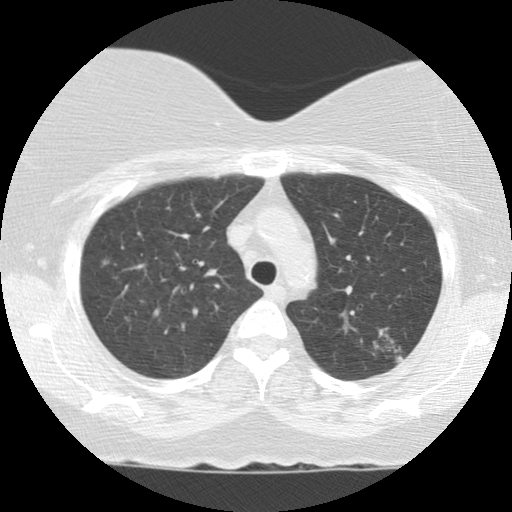
Chest CT (low-dose screening protocol), one axial image. Baseline annual screen. Lung window (W 1500 / L -600 HU). 2.5 mm slice thickness. Standard (soft-tissue) reconstruction kernel (STANDARD). Slice 27 of 123 in the series. Female participant, aged 56 years at enrolment. Current smoker at enrolment.
Expert-annotated lung lesion, box from (x=357, y=317) to (x=419, y=383) px. The screening reader recorded 4 non-calcified nodules or masses ≥4 mm on this exam (left upper lobe, left upper lobe, right upper lobe, left upper lobe); which of them this box marks is not recorded. Participant outcome: lung cancer diagnosed 798 days after this screen — adenocarcinoma, NOS, left upper lobe, moderately differentiated (G2), stage IA (AJCC 6th edition), 10 mm at pathology.